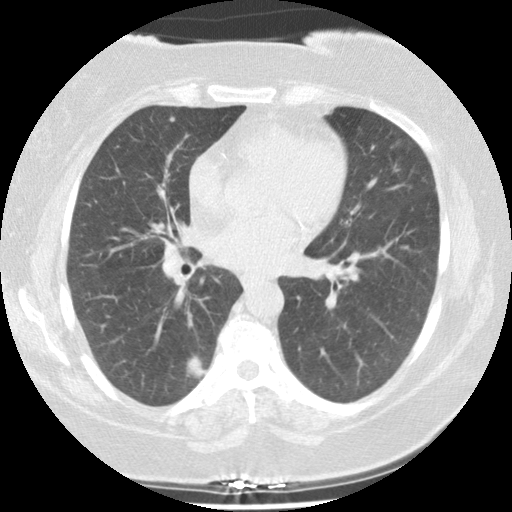
Chest CT (low-dose screening protocol), one axial image; second annual screen; lung window (W 1500 / L -600 HU); 2.5 mm slice thickness; 140 kVp. Female, age 58 years at enrolment. Current smoker at enrolment.
Expert reader's lesion annotation, box from (x=165, y=337) to (x=219, y=400) px. The screening reader recorded 4 non-calcified nodules or masses ≥4 mm on this exam (right lower lobe, right middle lobe, right upper lobe, right middle lobe); which of them this box marks is not recorded. Later outcome: lung cancer diagnosed 299 days after this screen — adenocarcinoma, NOS, right lower lobe, stage IIIA (AJCC 6th edition), 25 mm at pathology.